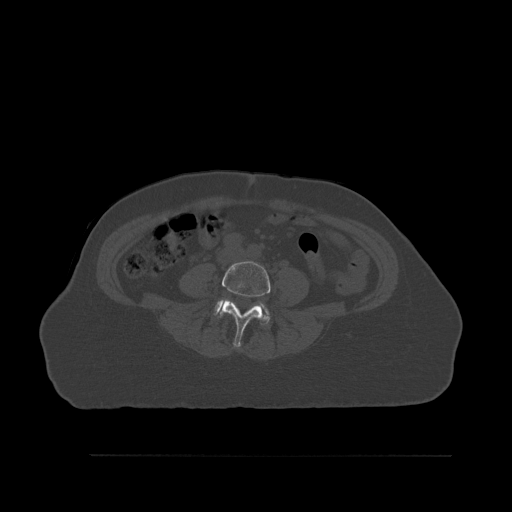
CT including the spine, one axial slice; position 204 of 527 along the scan axis; bone window (W 1800 / L 400 HU); 1.5 mm slice thickness; 512 × 512 image matrix, field of view 470 × 470 mm. Patient: female, 73 years. From the clinical record (not read from this slice): primary cancer: breast.
Structures marked on this image (semi-automatic segmentation, software-assisted and operator-edited):
- L4 vertebra: bounding box [x1, y1, x2, y2] px = [219, 261, 271, 347]
- L5 vertebra: [214, 299, 270, 325]